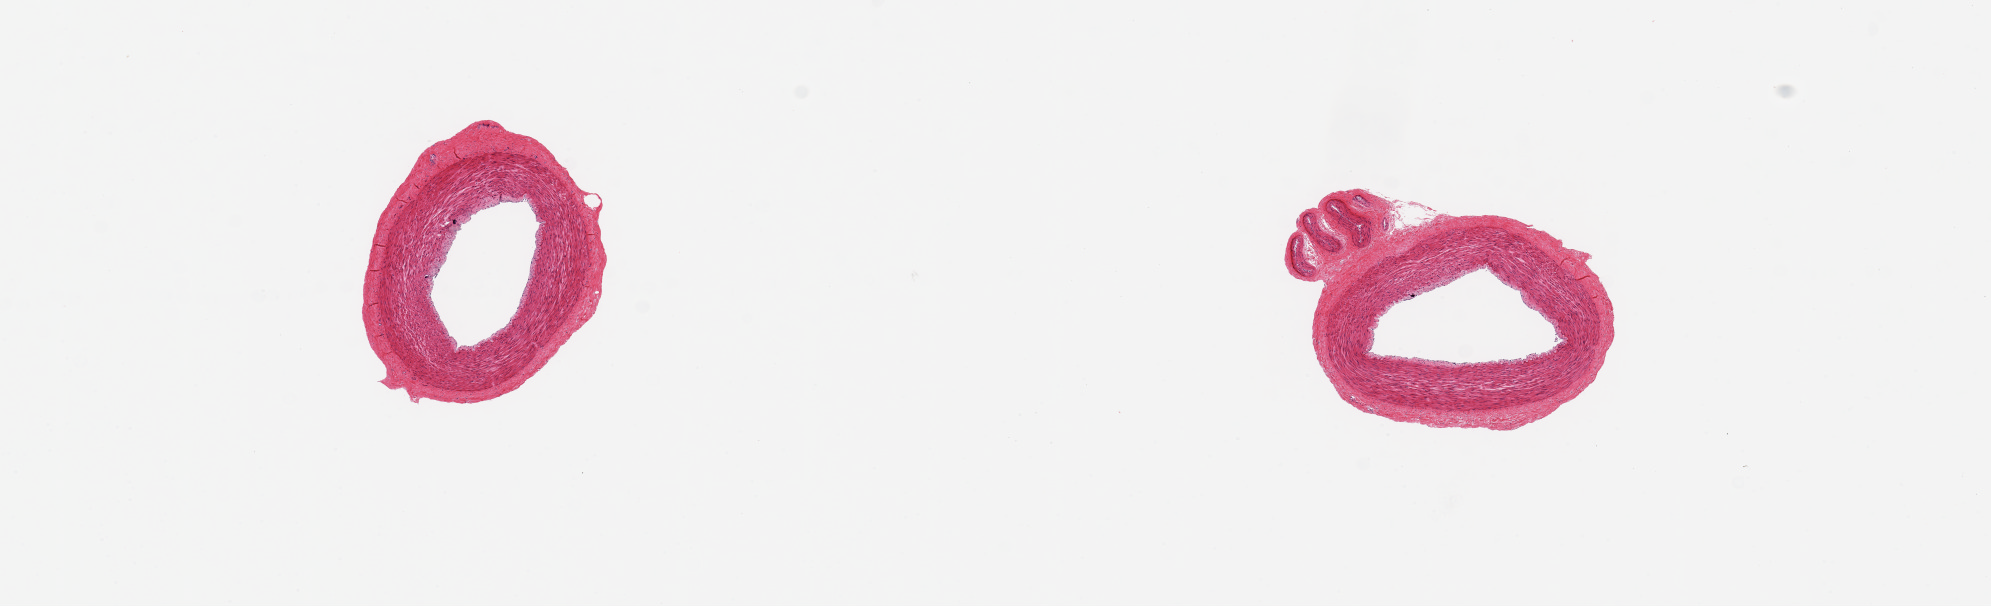
Digitized H&E-stained section, brightfield — a low-resolution overview of the entire scanned area, about 15.8 x 4.8 mm, PAXgene-fixed paraffin-embedded (PFPE) section, section of tibial artery (target tissue), tissue donor sample. Donor: male.
Reviewer comment on this tissue sample: 2 pieces ~2.5mm d. Good clean specimens; one has adherent nubbin of additiona vessel ~0.5mm d.